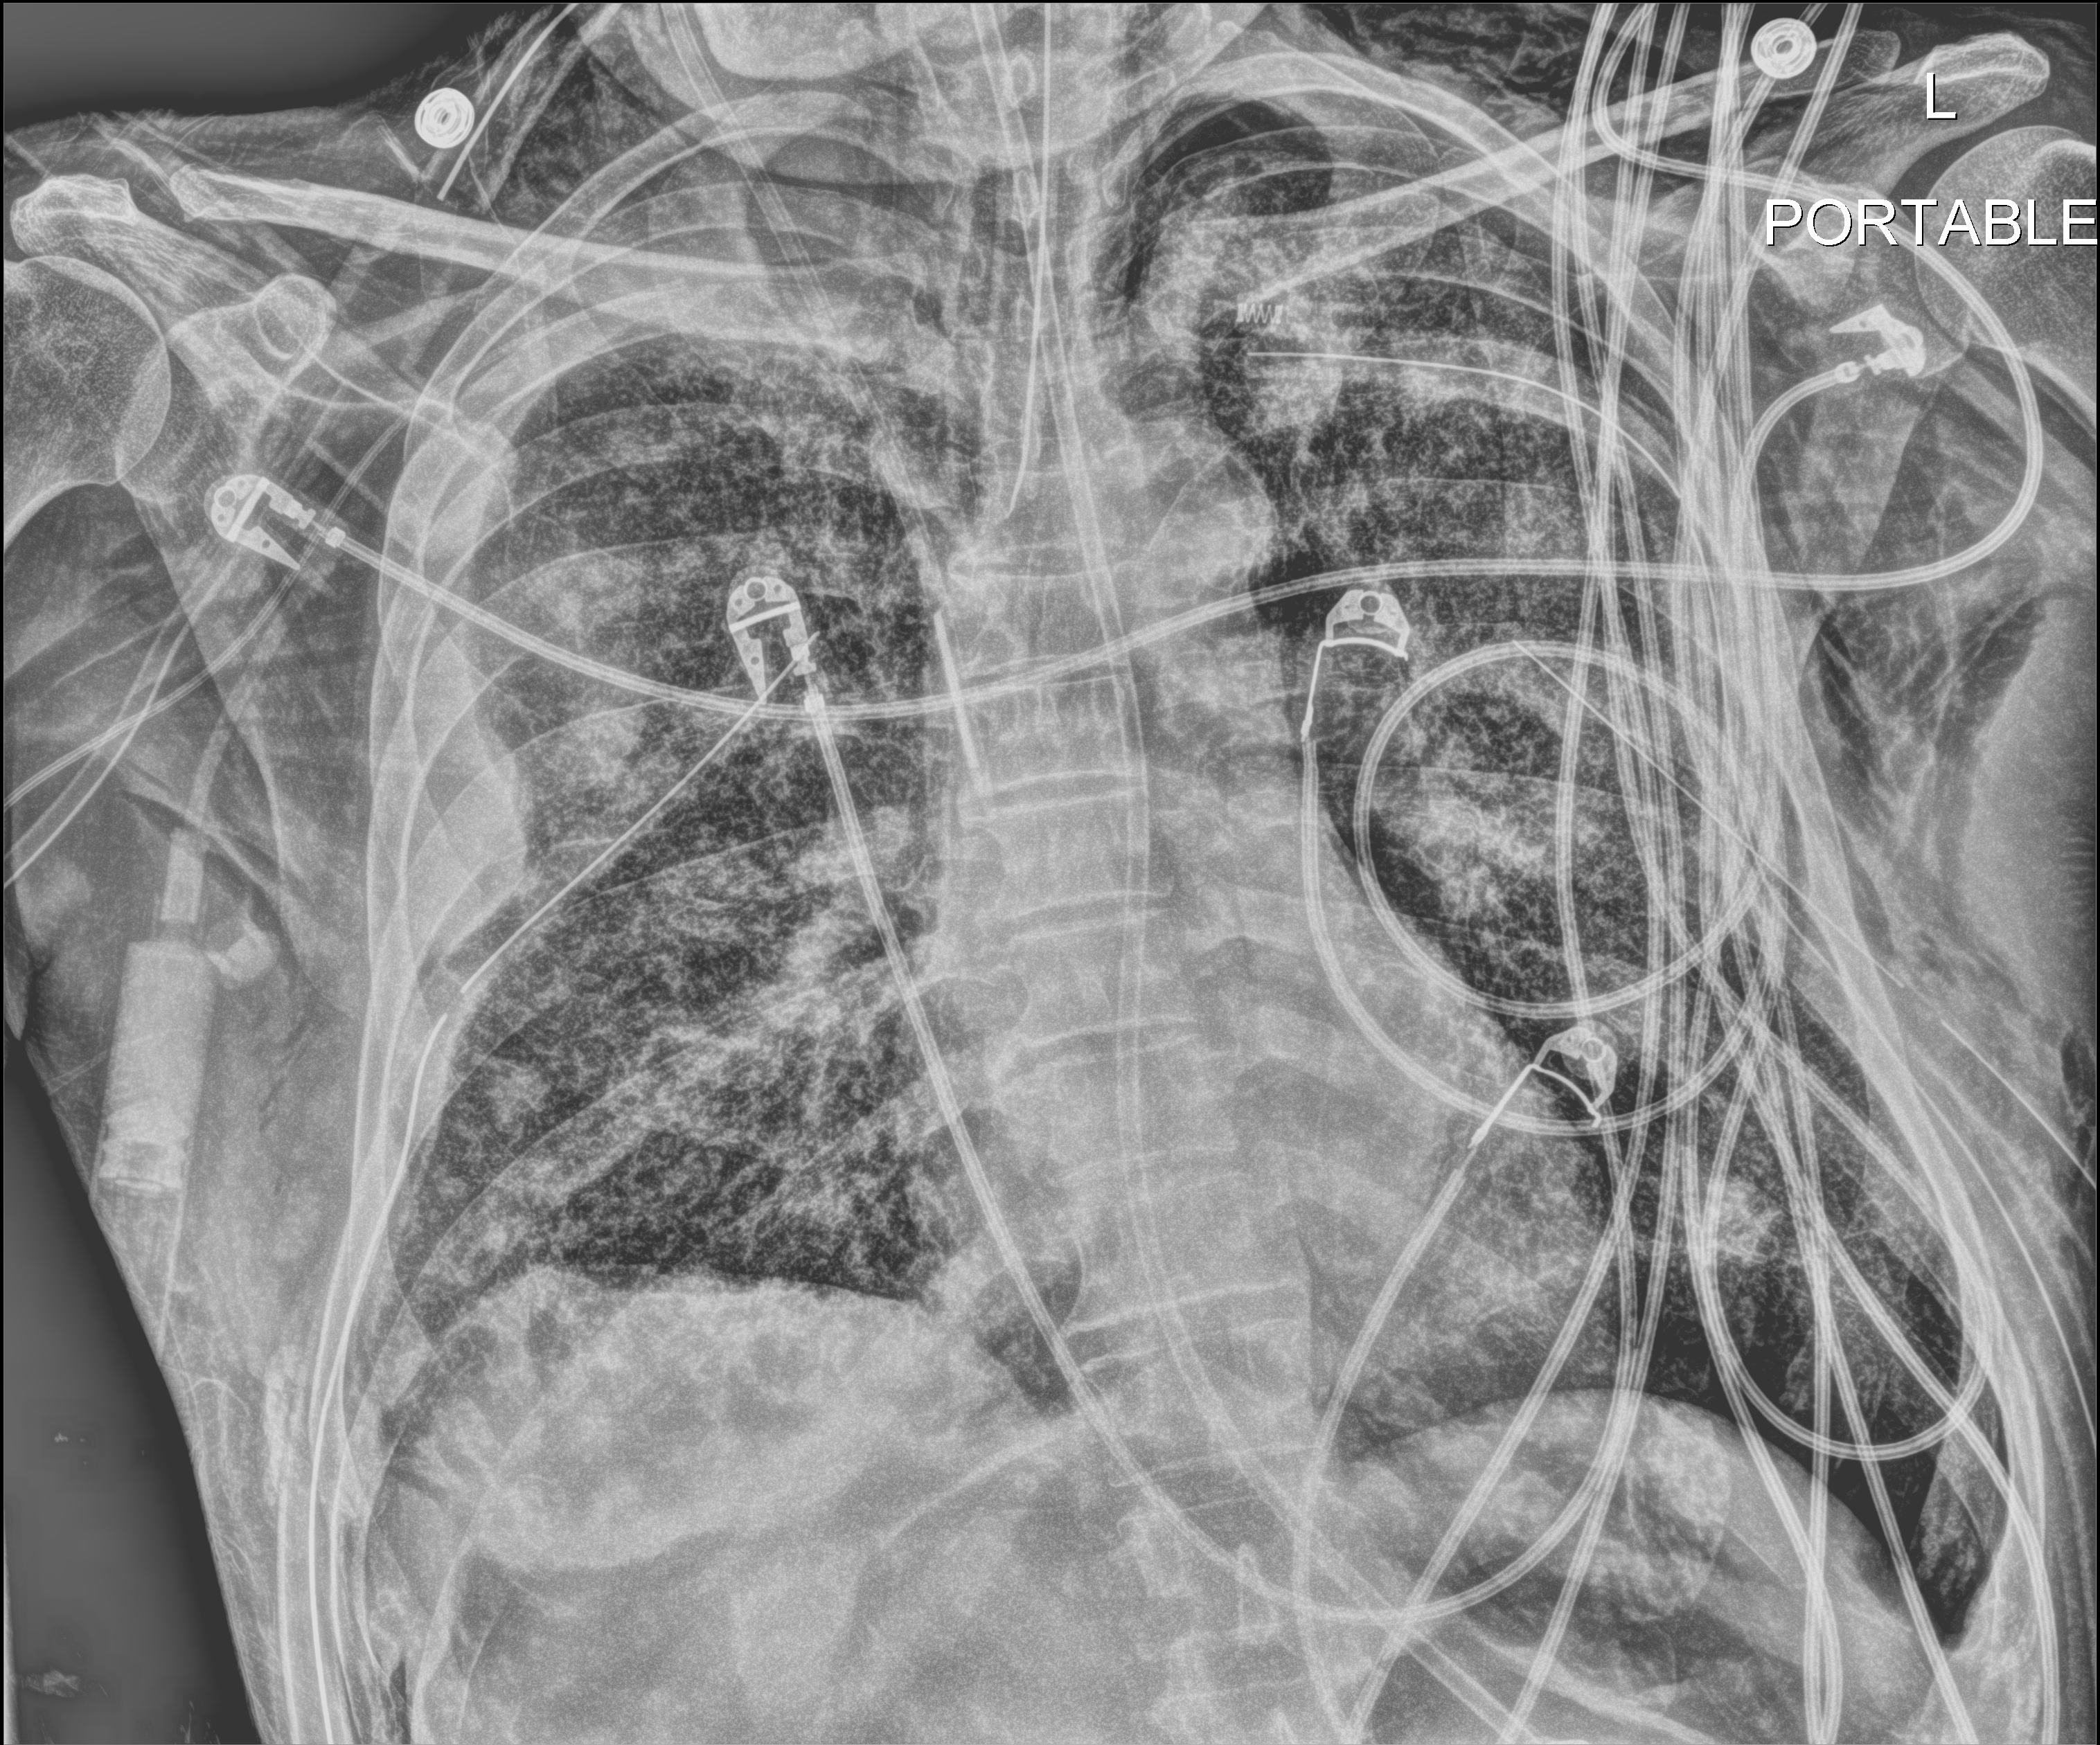
Portable chest radiograph, anteroposterior (AP) projection. Male patient hospitalised with COVID-19, age 18–59 years.
From the hospital-stay record, not from the radiograph (when in the stay this image was taken is not recorded): admitted to intensive care during this hospital stay: yes.